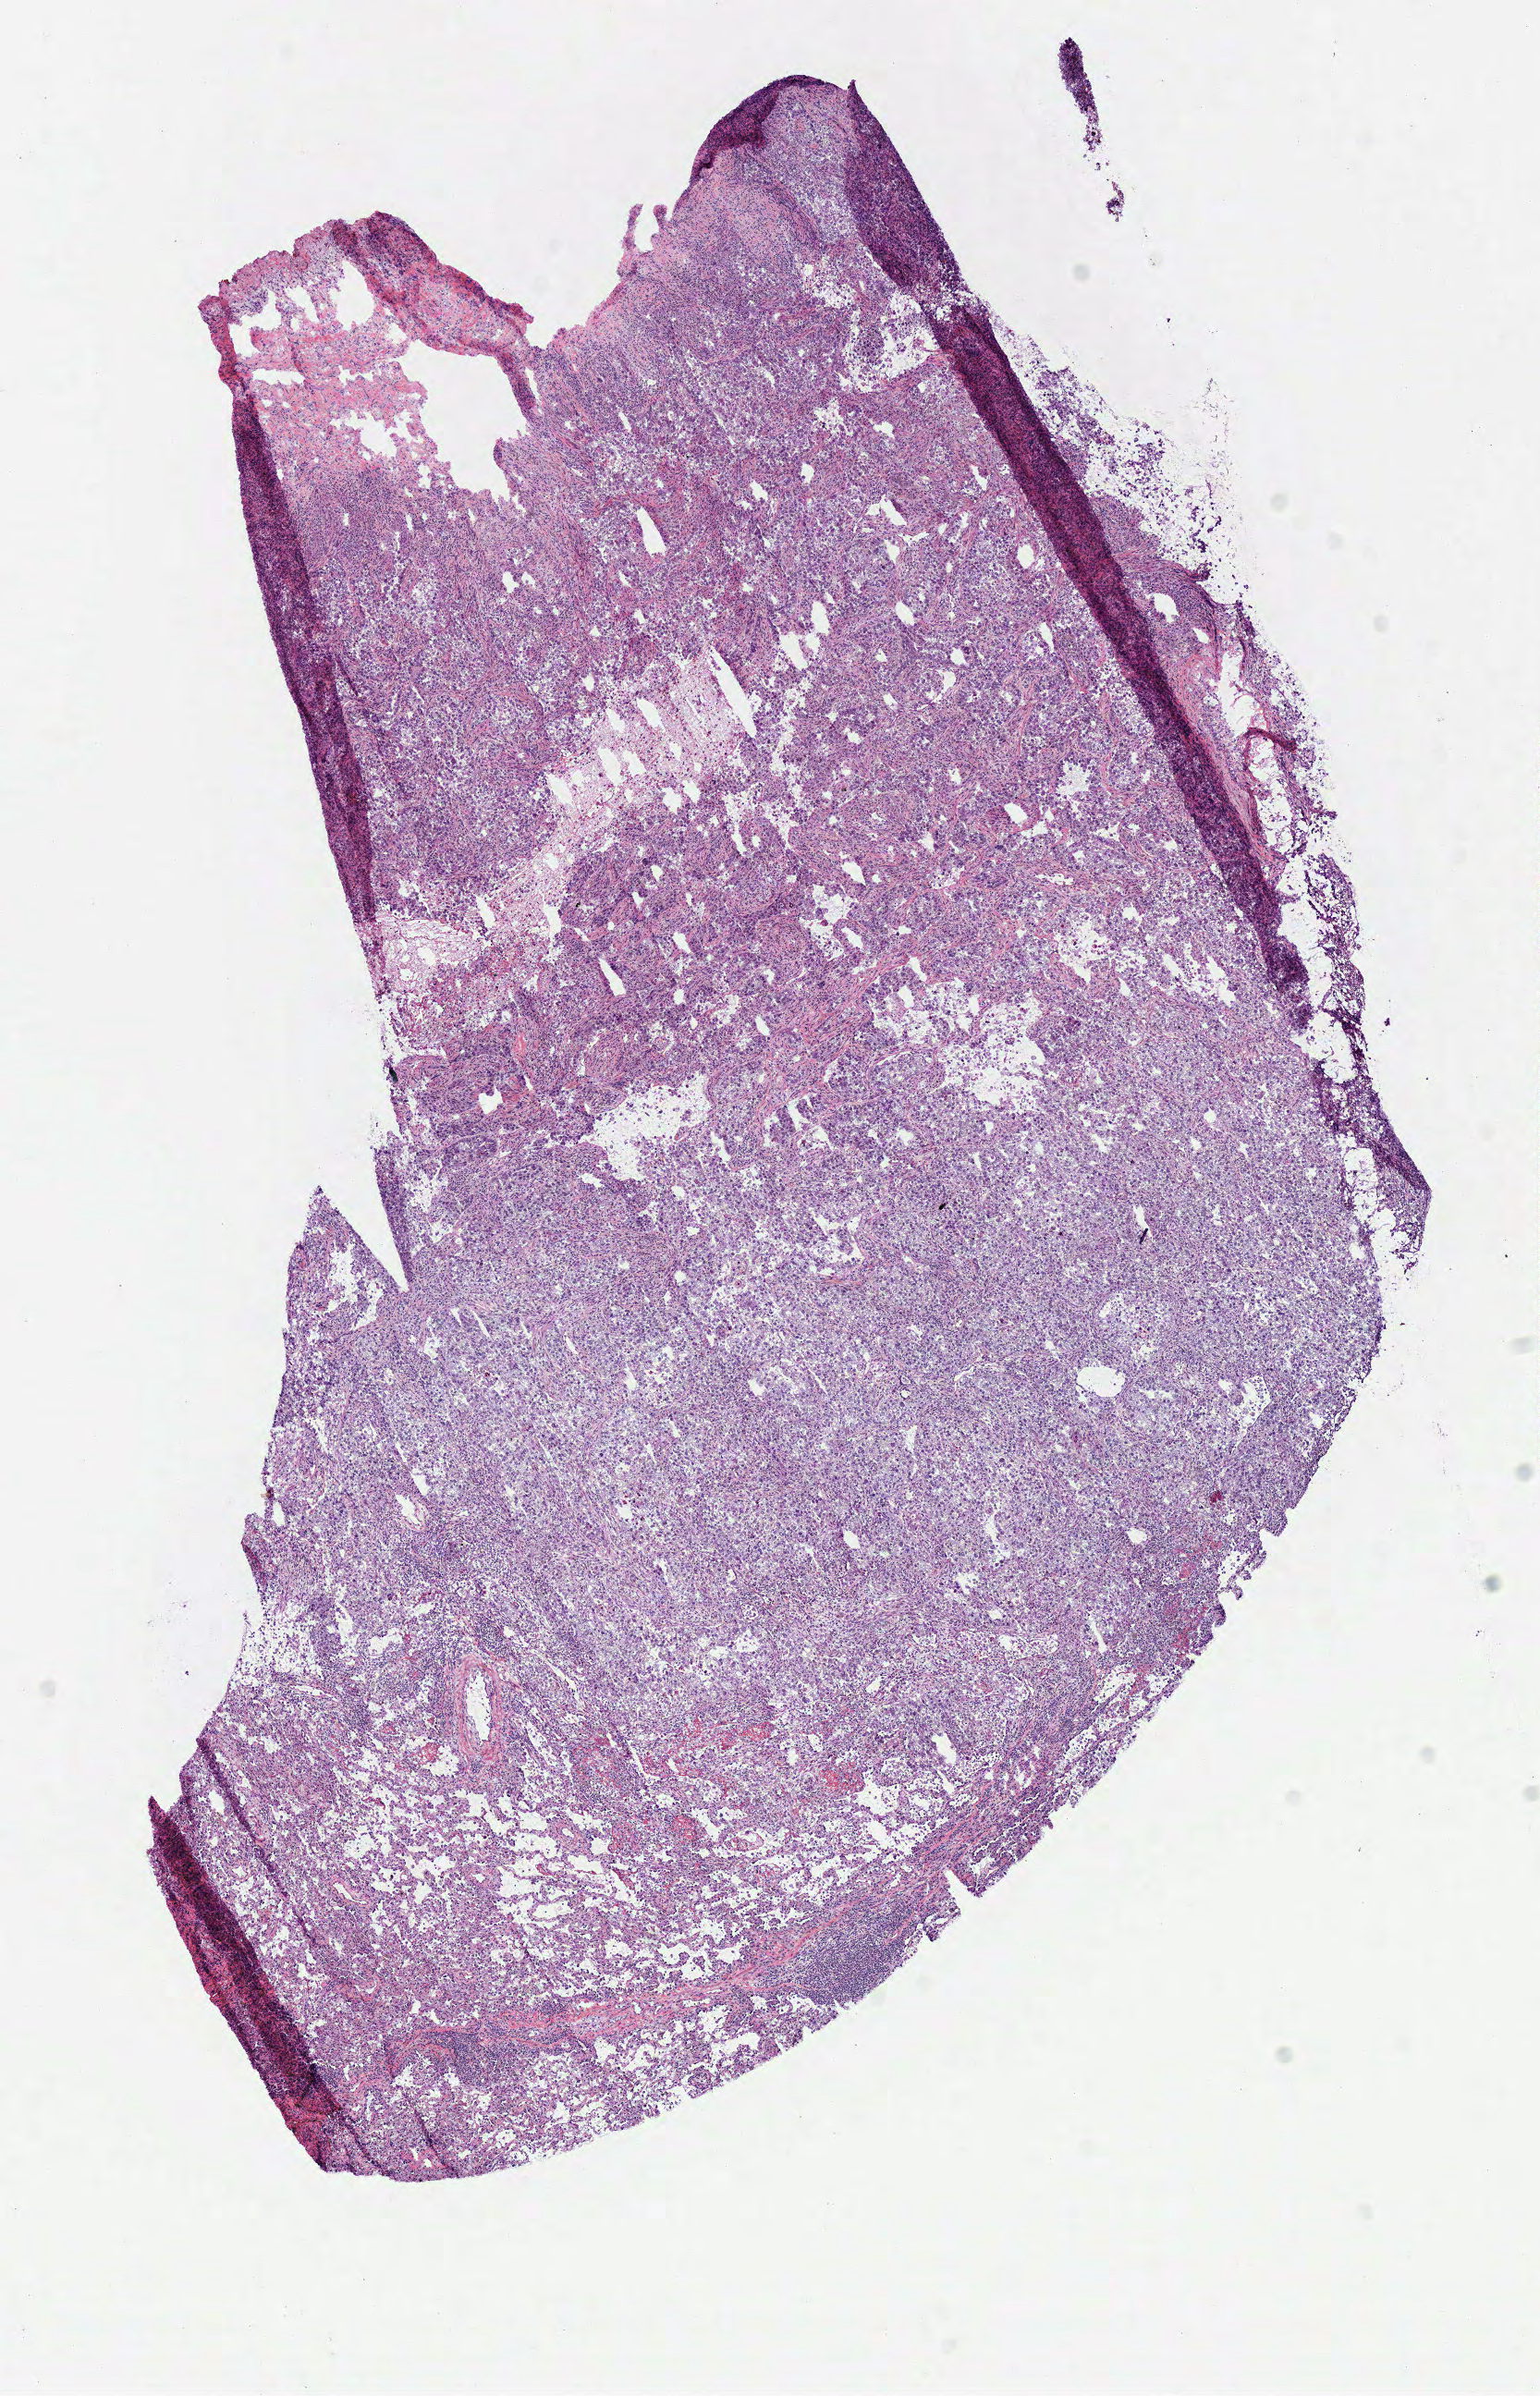
H&E-stained whole-slide image, low-resolution overview of the scanned area, about 6.6 x 10.2 mm, frozen section from the top of the tissue portion, primary tumour sample from the lung. Patient sex: male.
Histologic diagnosis: Squamous cell carcinoma, NOS (upper lobe, lung).